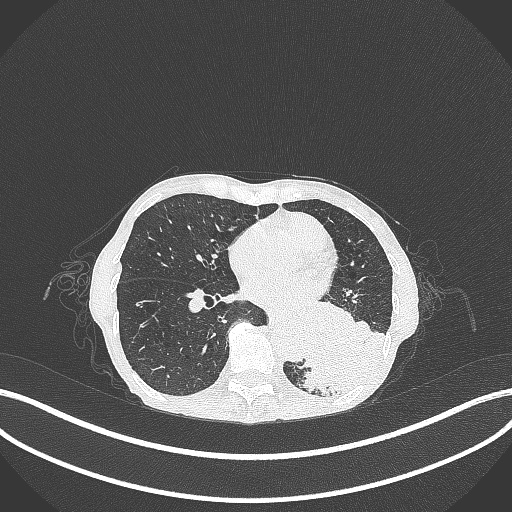
Chest CT, one axial slice. Slice 109 of 347 in the series (ordered by position). Reconstruction kernel B70f. Lung window (W 1500 / L -600 HU). 1 mm slice thickness. 512 × 512 image matrix. Female patient, age 70 years. Case-level facts recorded for this patient, not image findings: clinical TNM (as recorded): T3 N0 M0.
Annotated regions visible in this slice (rectangle marked by the reading radiologist):
- lung tumour (recorded histology: small cell carcinoma): bounding box <290,307,386,402> (left, top, right, bottom; pixels)